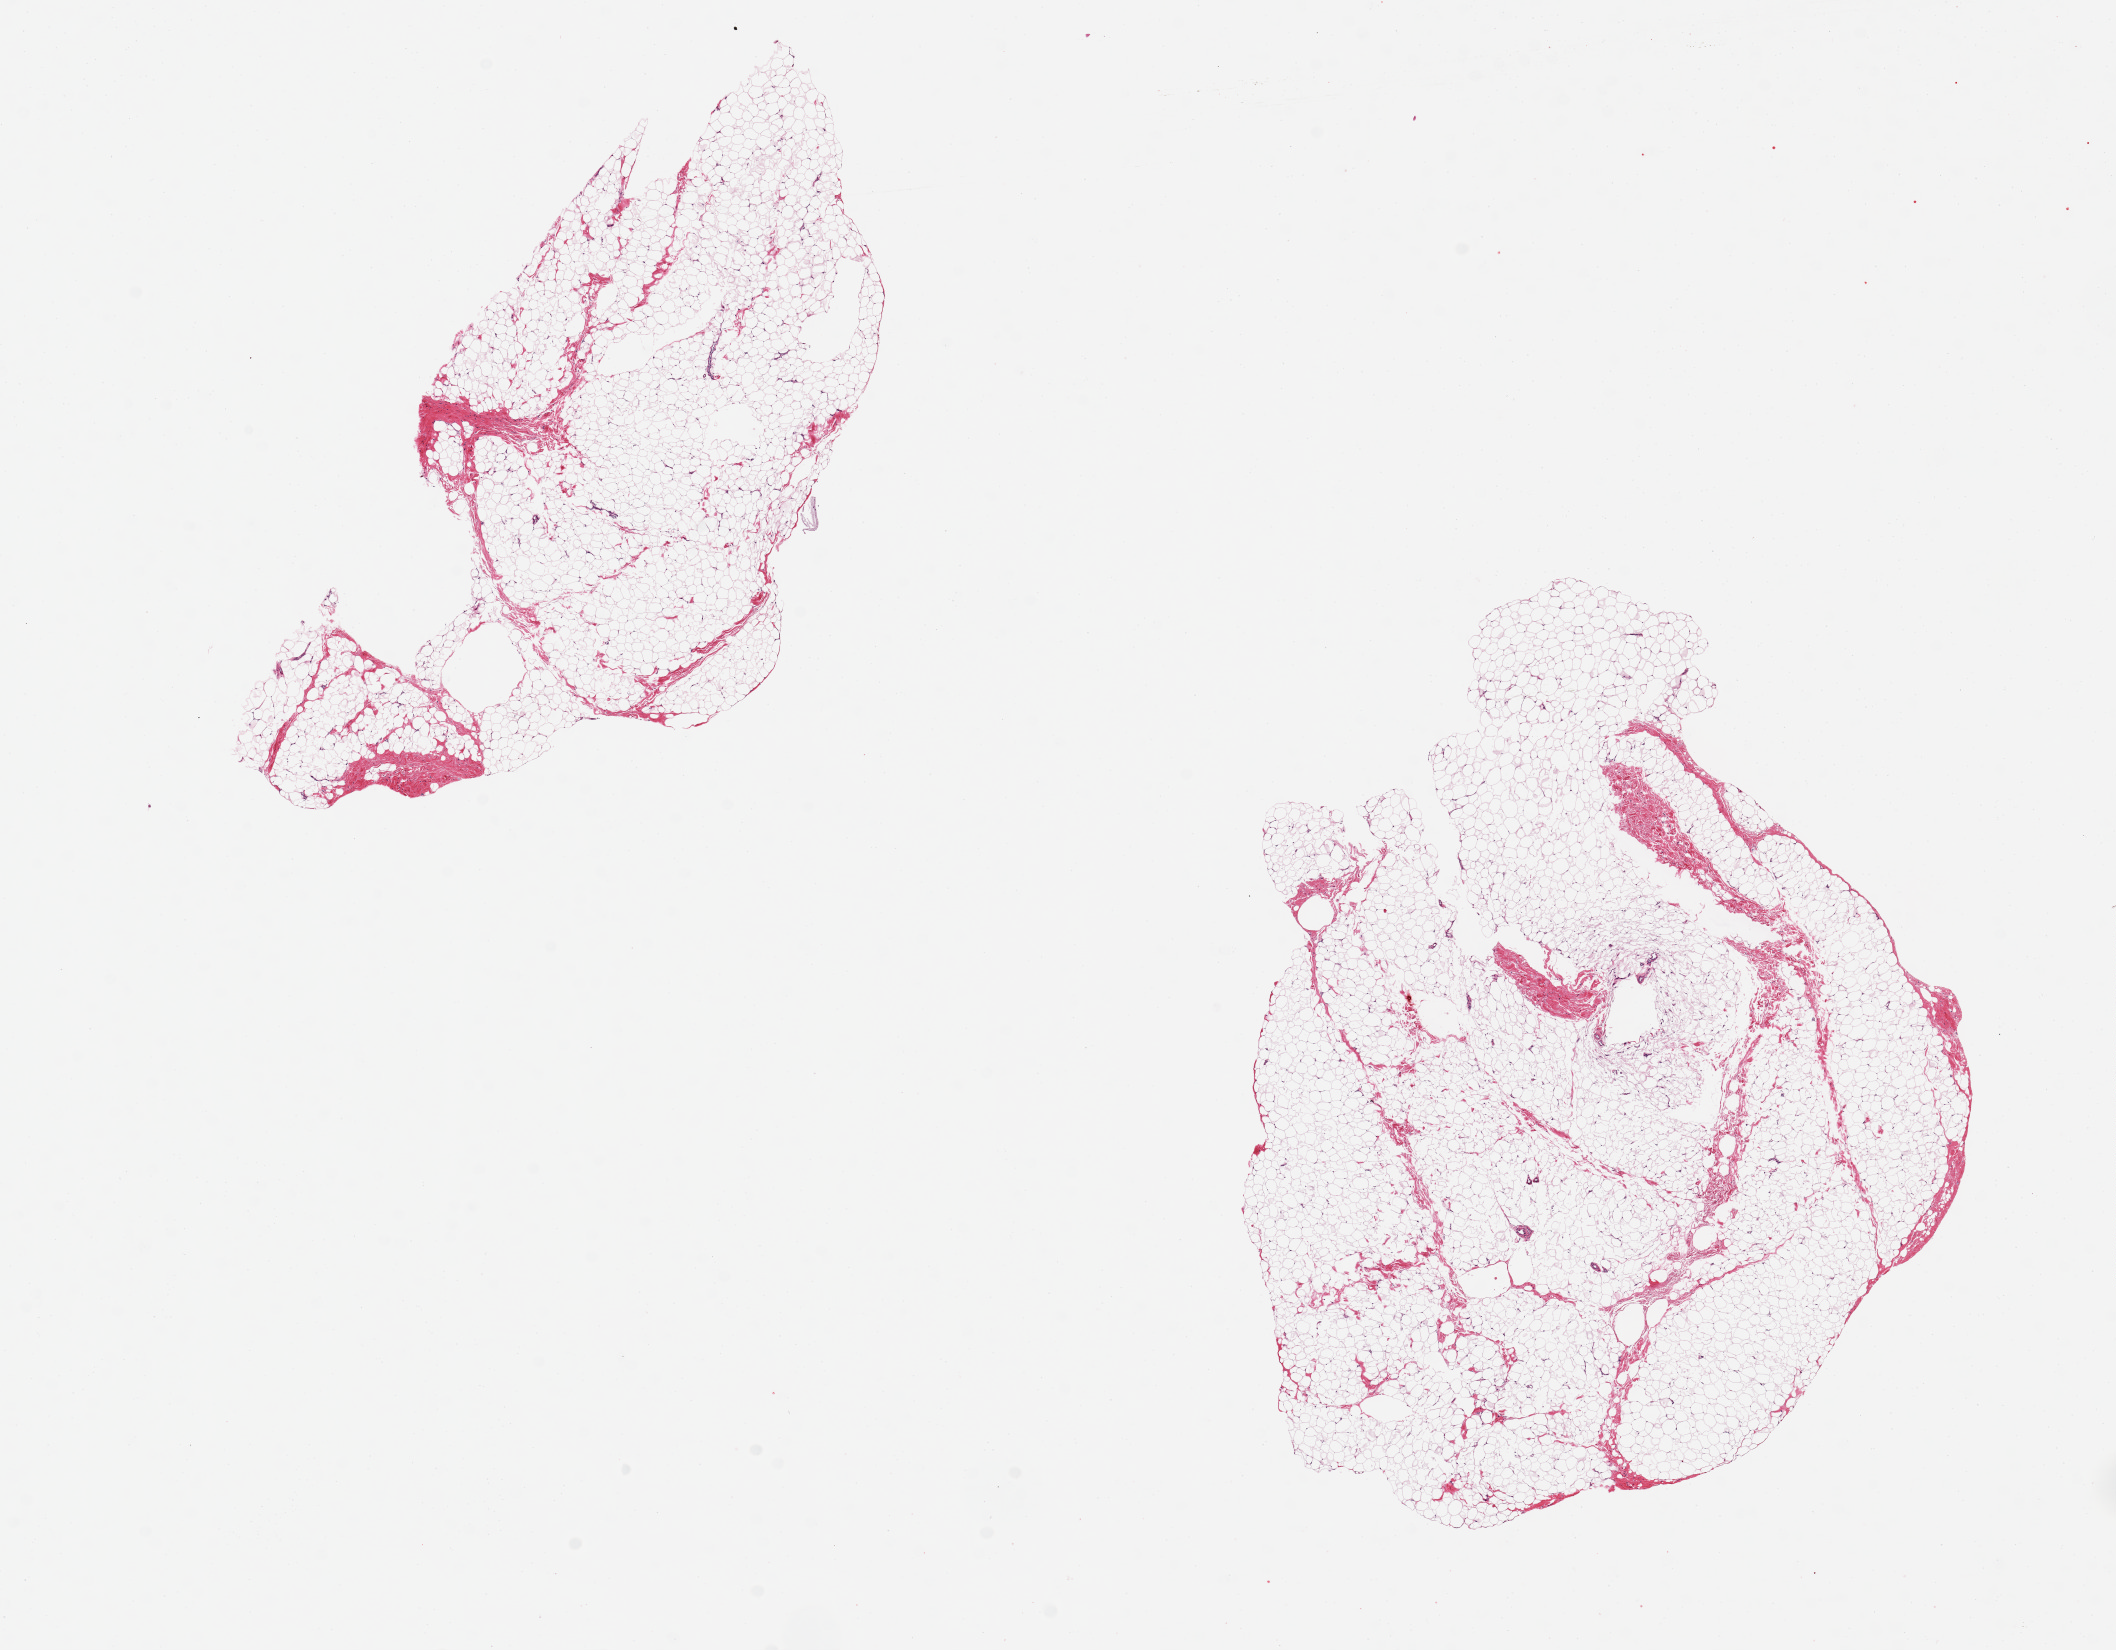
Whole-slide image, haematoxylin and eosin stain, a low-resolution overview of the entire scanned area, about 16.7 x 13.0 mm (acquisition: 20x scan); PAXgene-fixed, paraffin-embedded tissue; sampled site (target tissue): breast; tissue donor sample. Donor sex: male.
Pathologist's review note for this sample: 2 pieces ~7x4mm. Fibroadipose tissue only, no ductal elements seen.